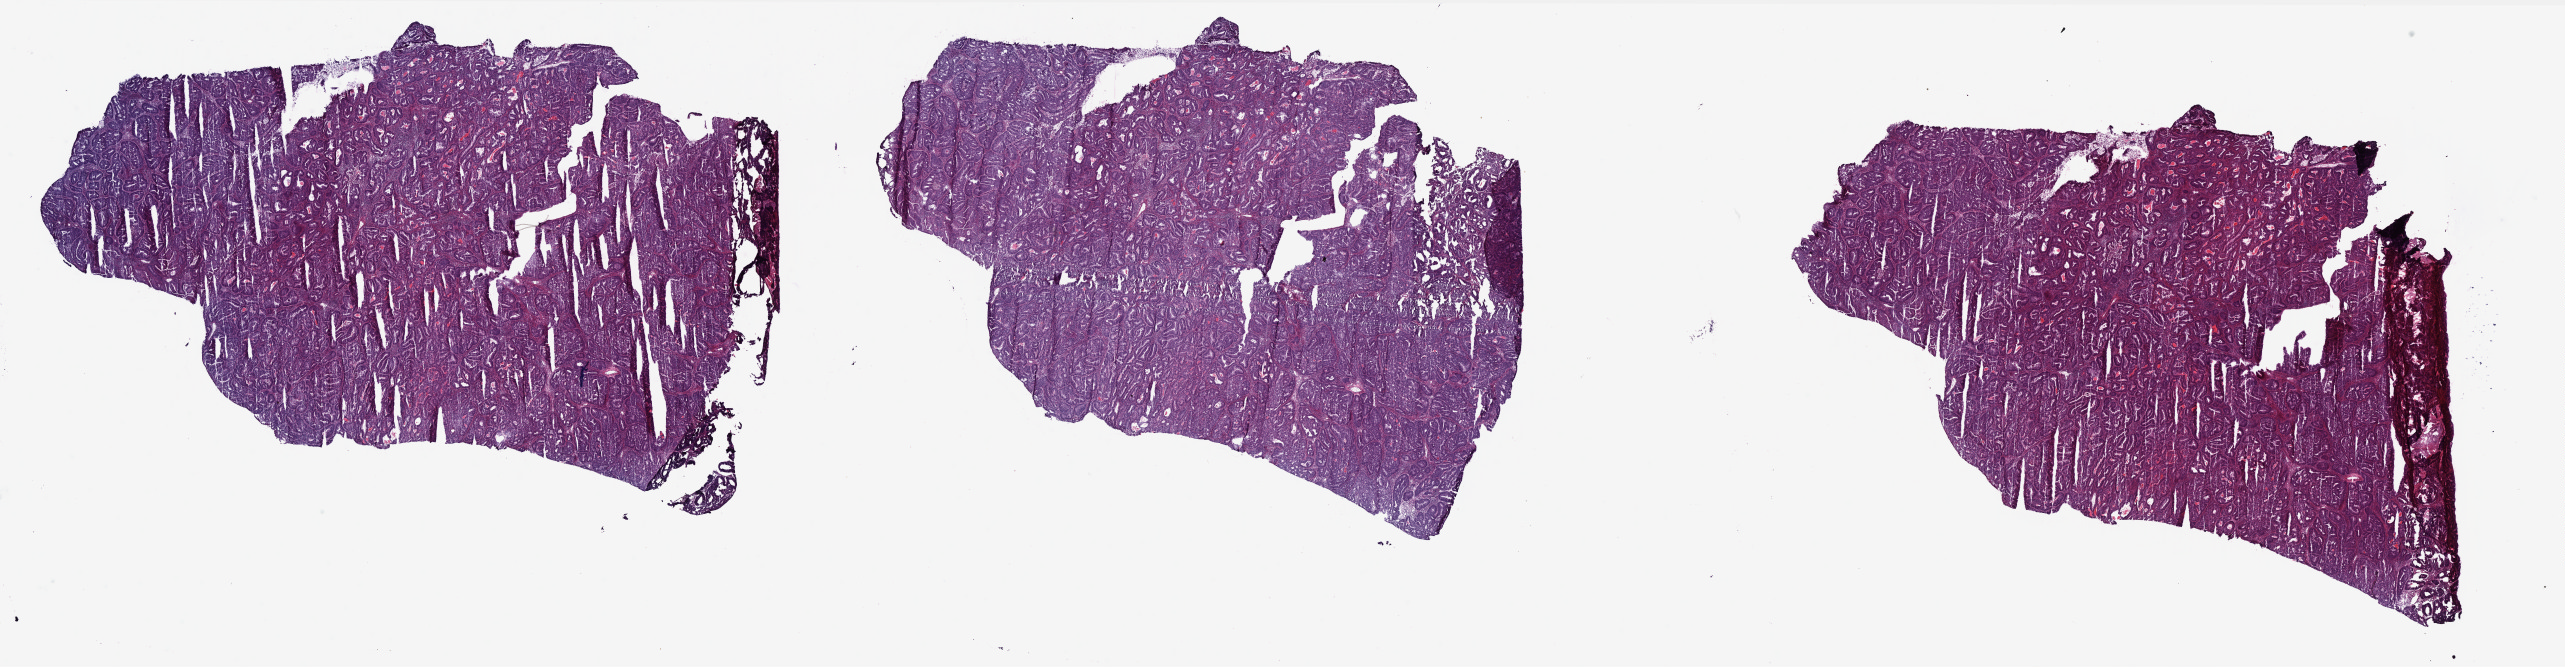
H&E whole-slide image, low-resolution overview of the scanned area, about 41.1 x 10.7 mm. Frozen section from the top of the tissue portion. Primary tumour sample from the uterus. Female, age 57 years at initial diagnosis. Histologic grade: G1 (well differentiated). Composition of this section per pathologist review: tumour cells 75%, tumour nuclei 75%, normal cells 0%, stromal cells 25%, necrosis 0%. Infiltration values recorded for this section: lymphocyte infiltration 0%, monocyte infiltration 0%, neutrophil infiltration 0%.
FIGO stage: IB. Lymph nodes positive (case pathology): 0 of 4 examined. Pathologic diagnosis: Endometrioid adenocarcinoma, NOS (endometrium).